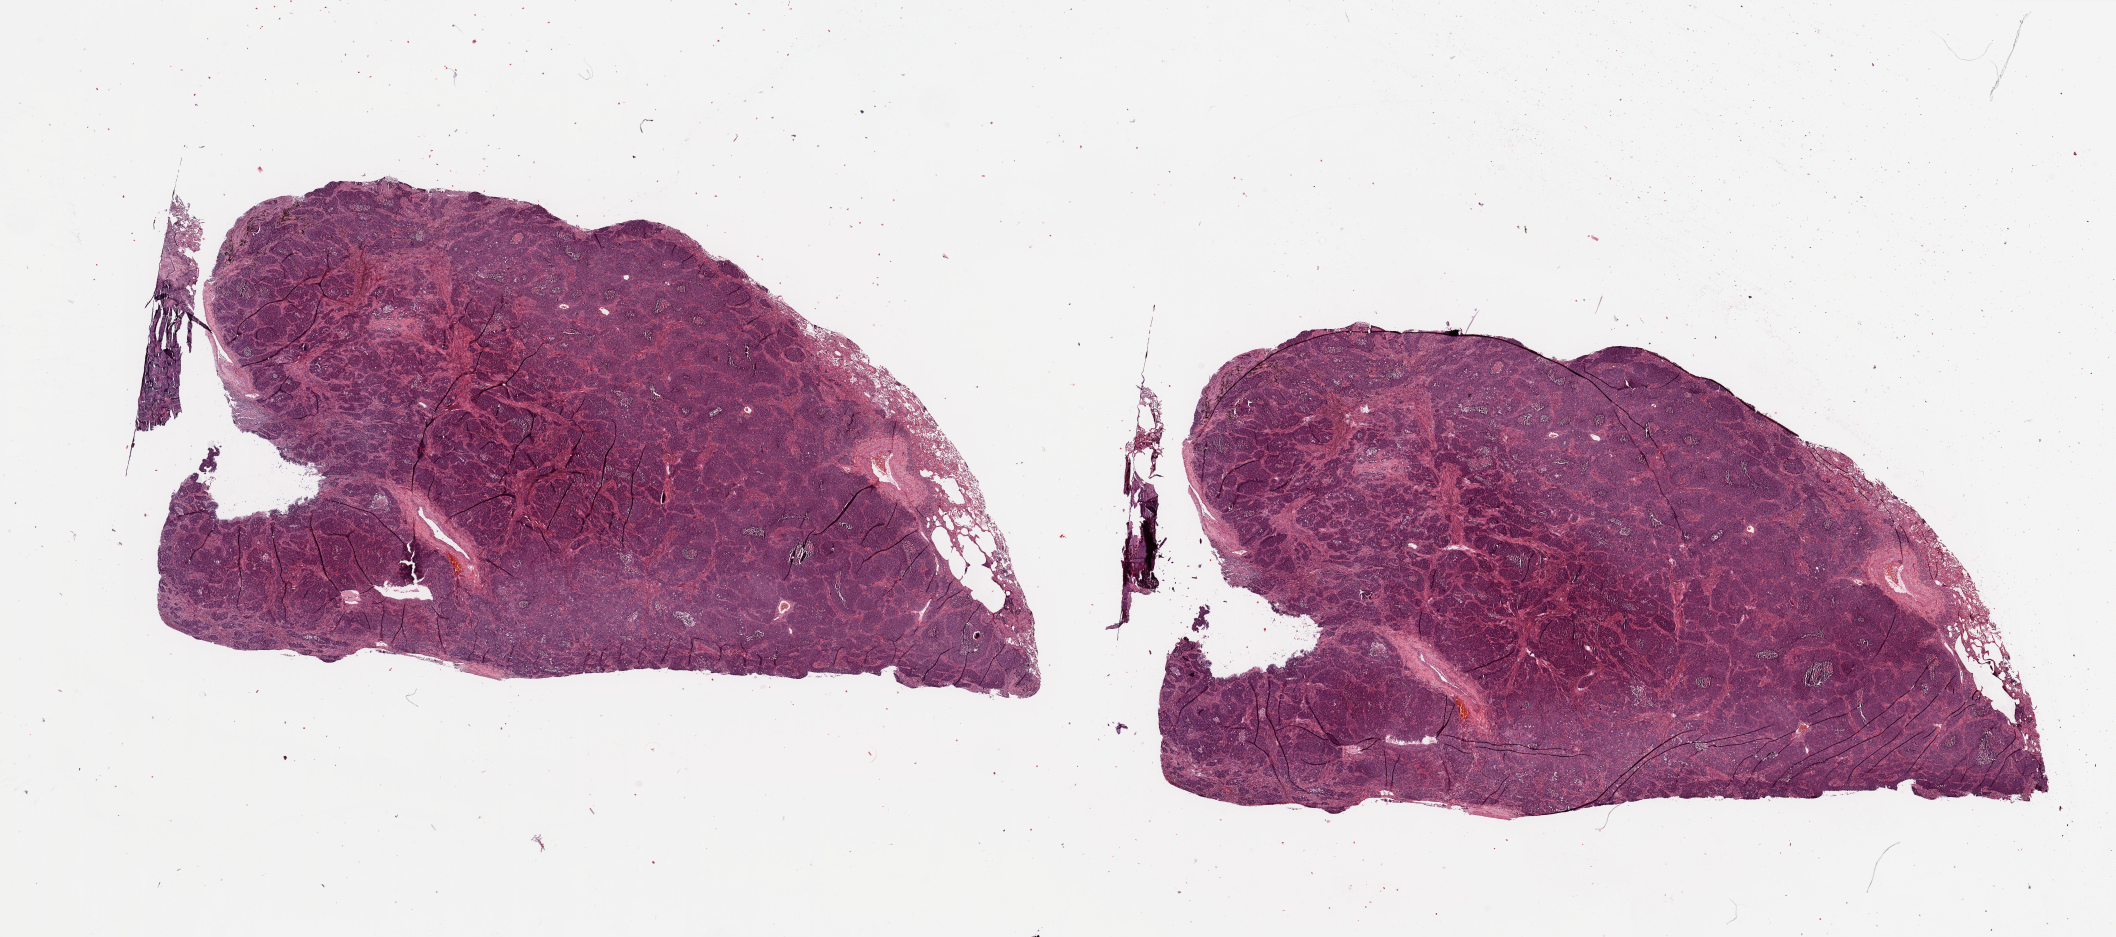
Digitized Hematoxylin and eosin (H&E) stained tissue section (whole slide) — whole scanned area (about 33.5 x 14.8 mm) shown as a low-resolution overview. Tumour tissue sample, sampled site: lung. Male, 61 y/o. Slide review estimates, as recorded: tumour nuclei 80%, necrosis 5%.
Histologic diagnosis: Squamous cell carcinoma, NOS.